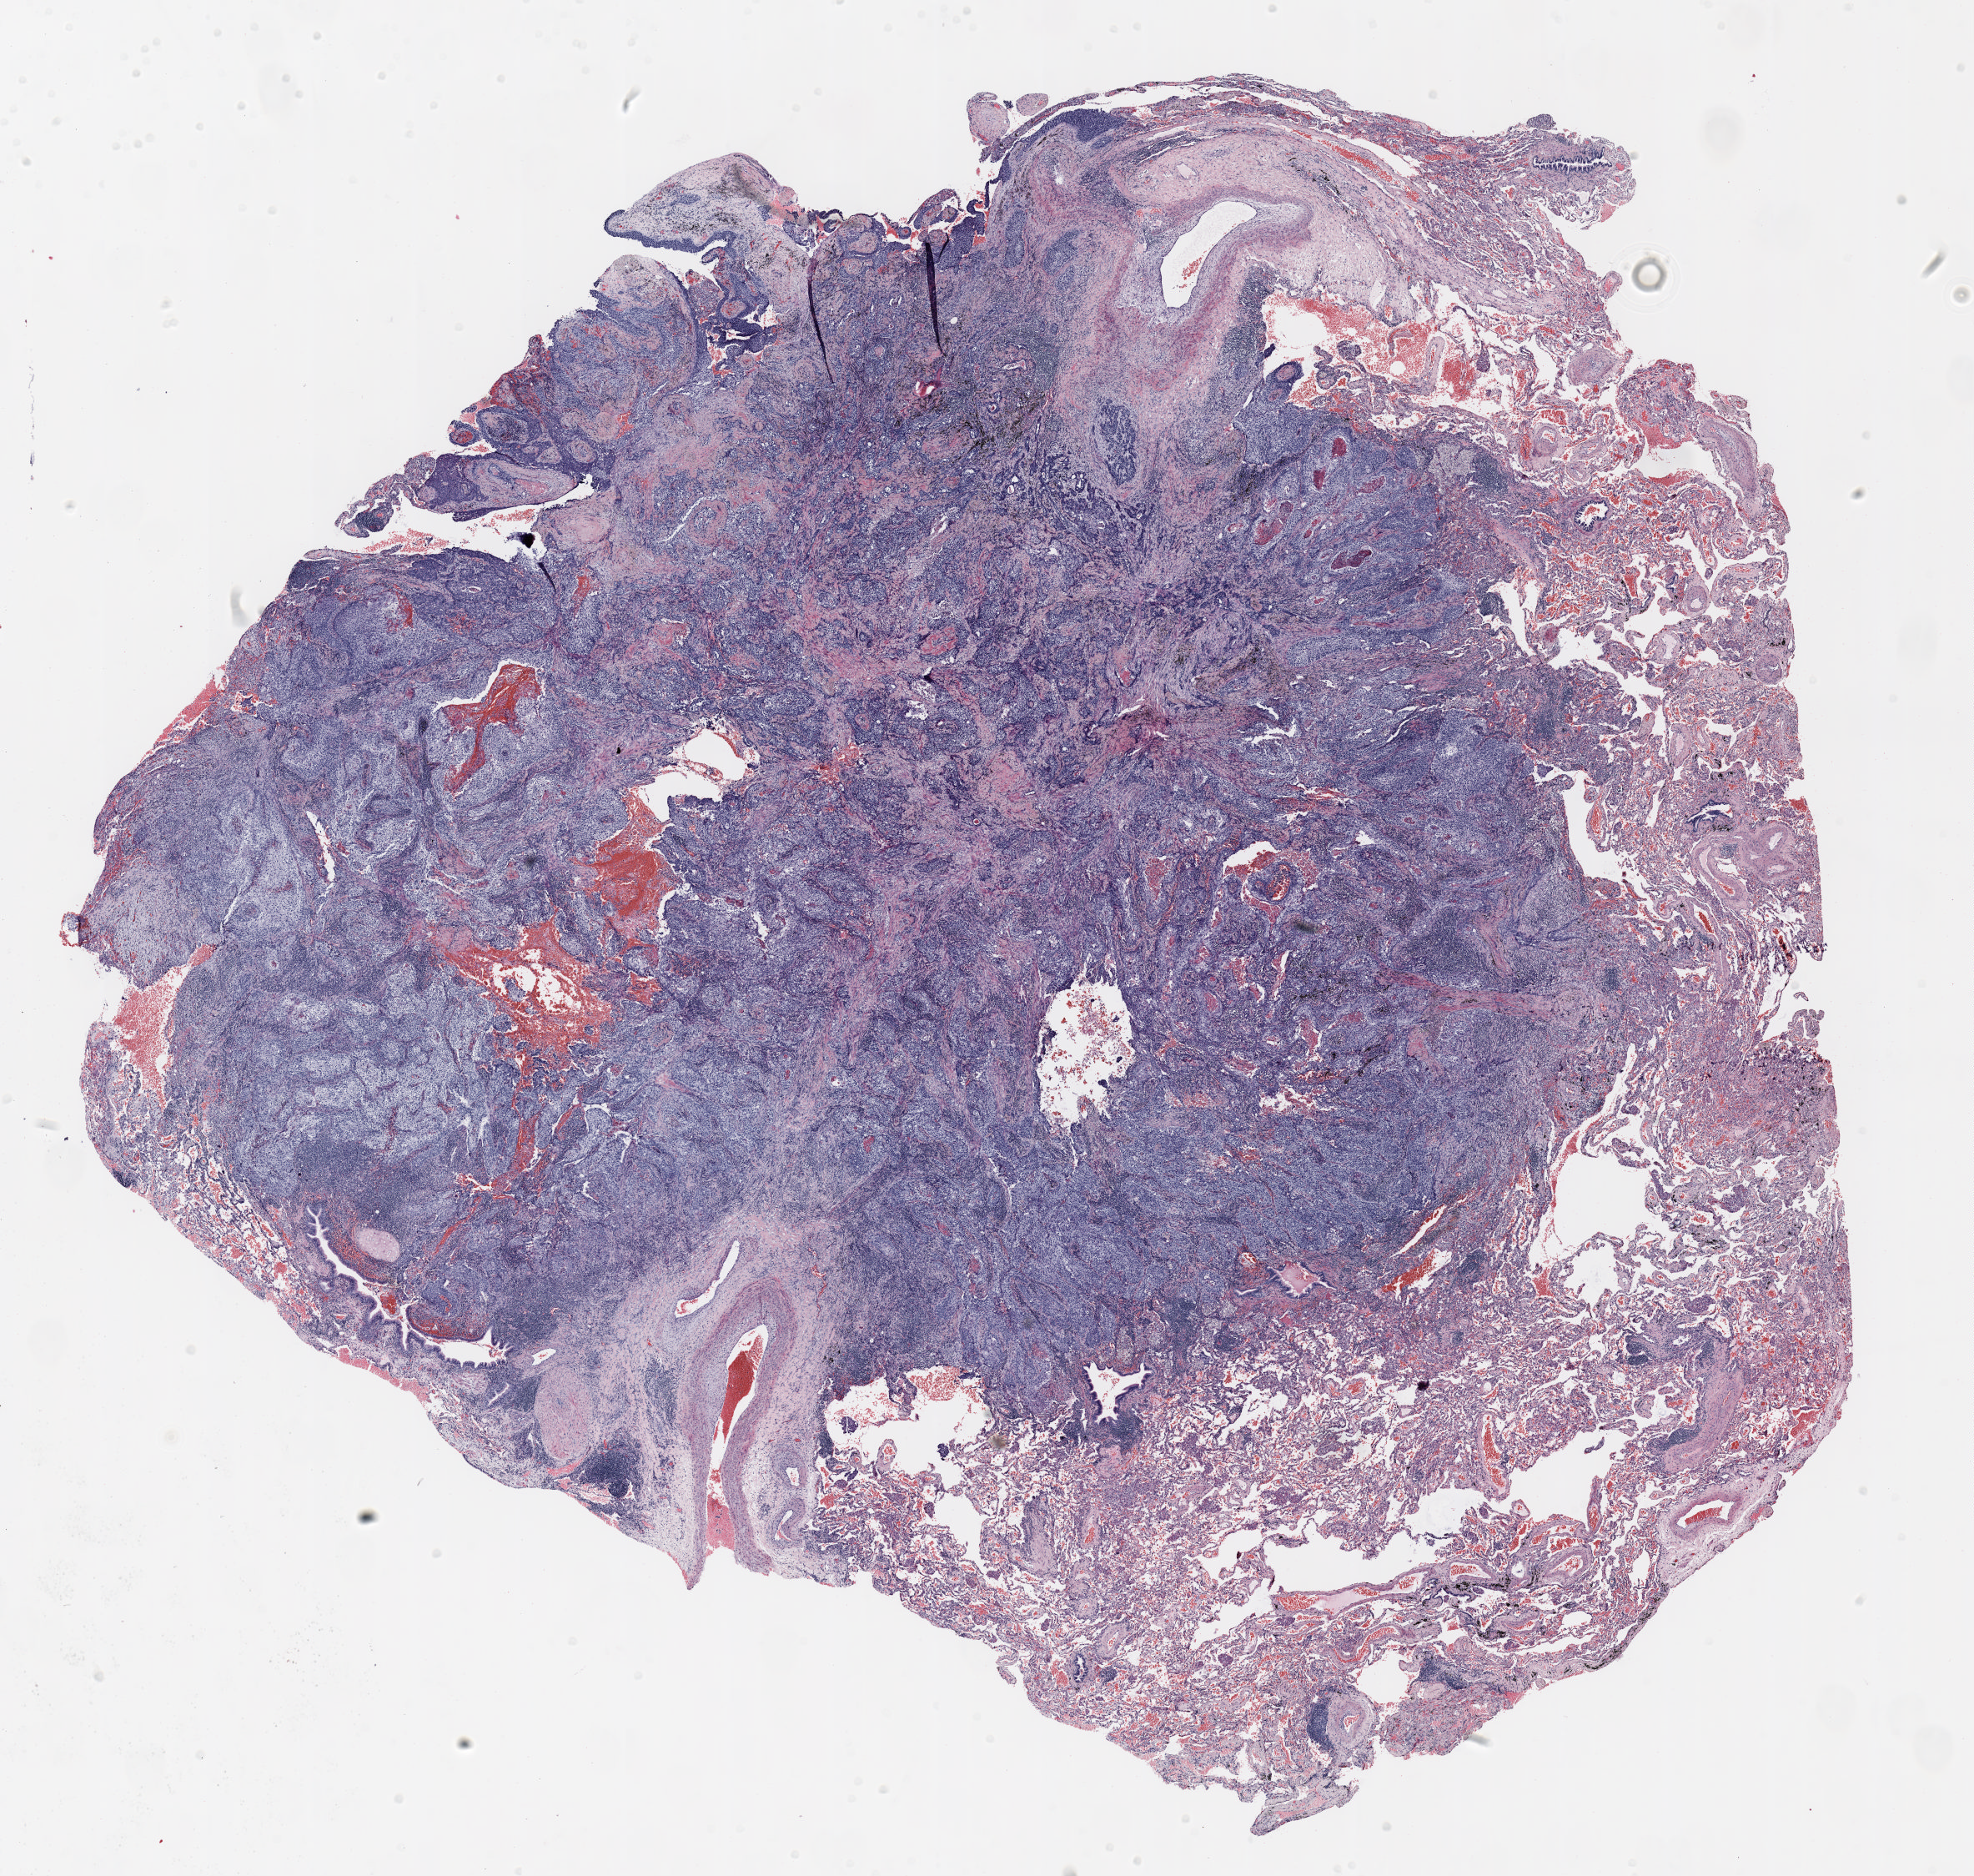
H&E-stained whole-slide image — whole scanned area (about 19.0 x 18.1 mm, acquisition: 20x scan) shown as a low-resolution overview. Formalin-fixed paraffin-embedded (FFPE) section. Lung tissue. Male, age 58 at enrolment. Grade: moderately differentiated (G2).
Primary tumour location (clinical record): right upper lobe. Participant's lung-cancer diagnosis: Squamous cell carcinoma, NOS (ICD-O-3 8070/3). Stage (AJCC 6th edition): IB. Tumour size (pathology): 18 mm.